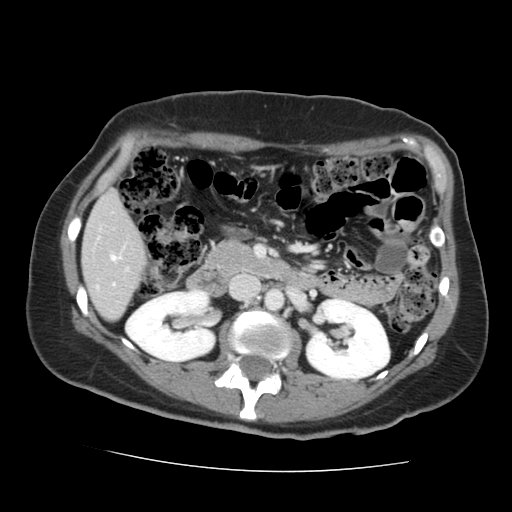
Contrast-enhanced abdominal CT, one axial slice. Slice 62 of 144 in the series (ordered by position). Intravenous contrast given. Soft-tissue window (W 400 / L 40 HU). 512 × 512 image matrix, field of view 333 × 333 mm. Female patient, age 46 years. From the clinical record (not read from this slice): diagnosis: colorectal cancer liver metastases, imaged before liver resection; multiple liver metastases: no; largest metastasis: 2.8 cm; disease in both lobes: no.
Outlined on this slice (manually delineated by an expert):
- liver: bounding box <83,194,144,319> (left, top, right, bottom; pixels)
- planned liver remnant (the part of the liver to remain after resection): <83,194,144,299>
- portal vein (with intrahepatic branches): <111,256,118,261>